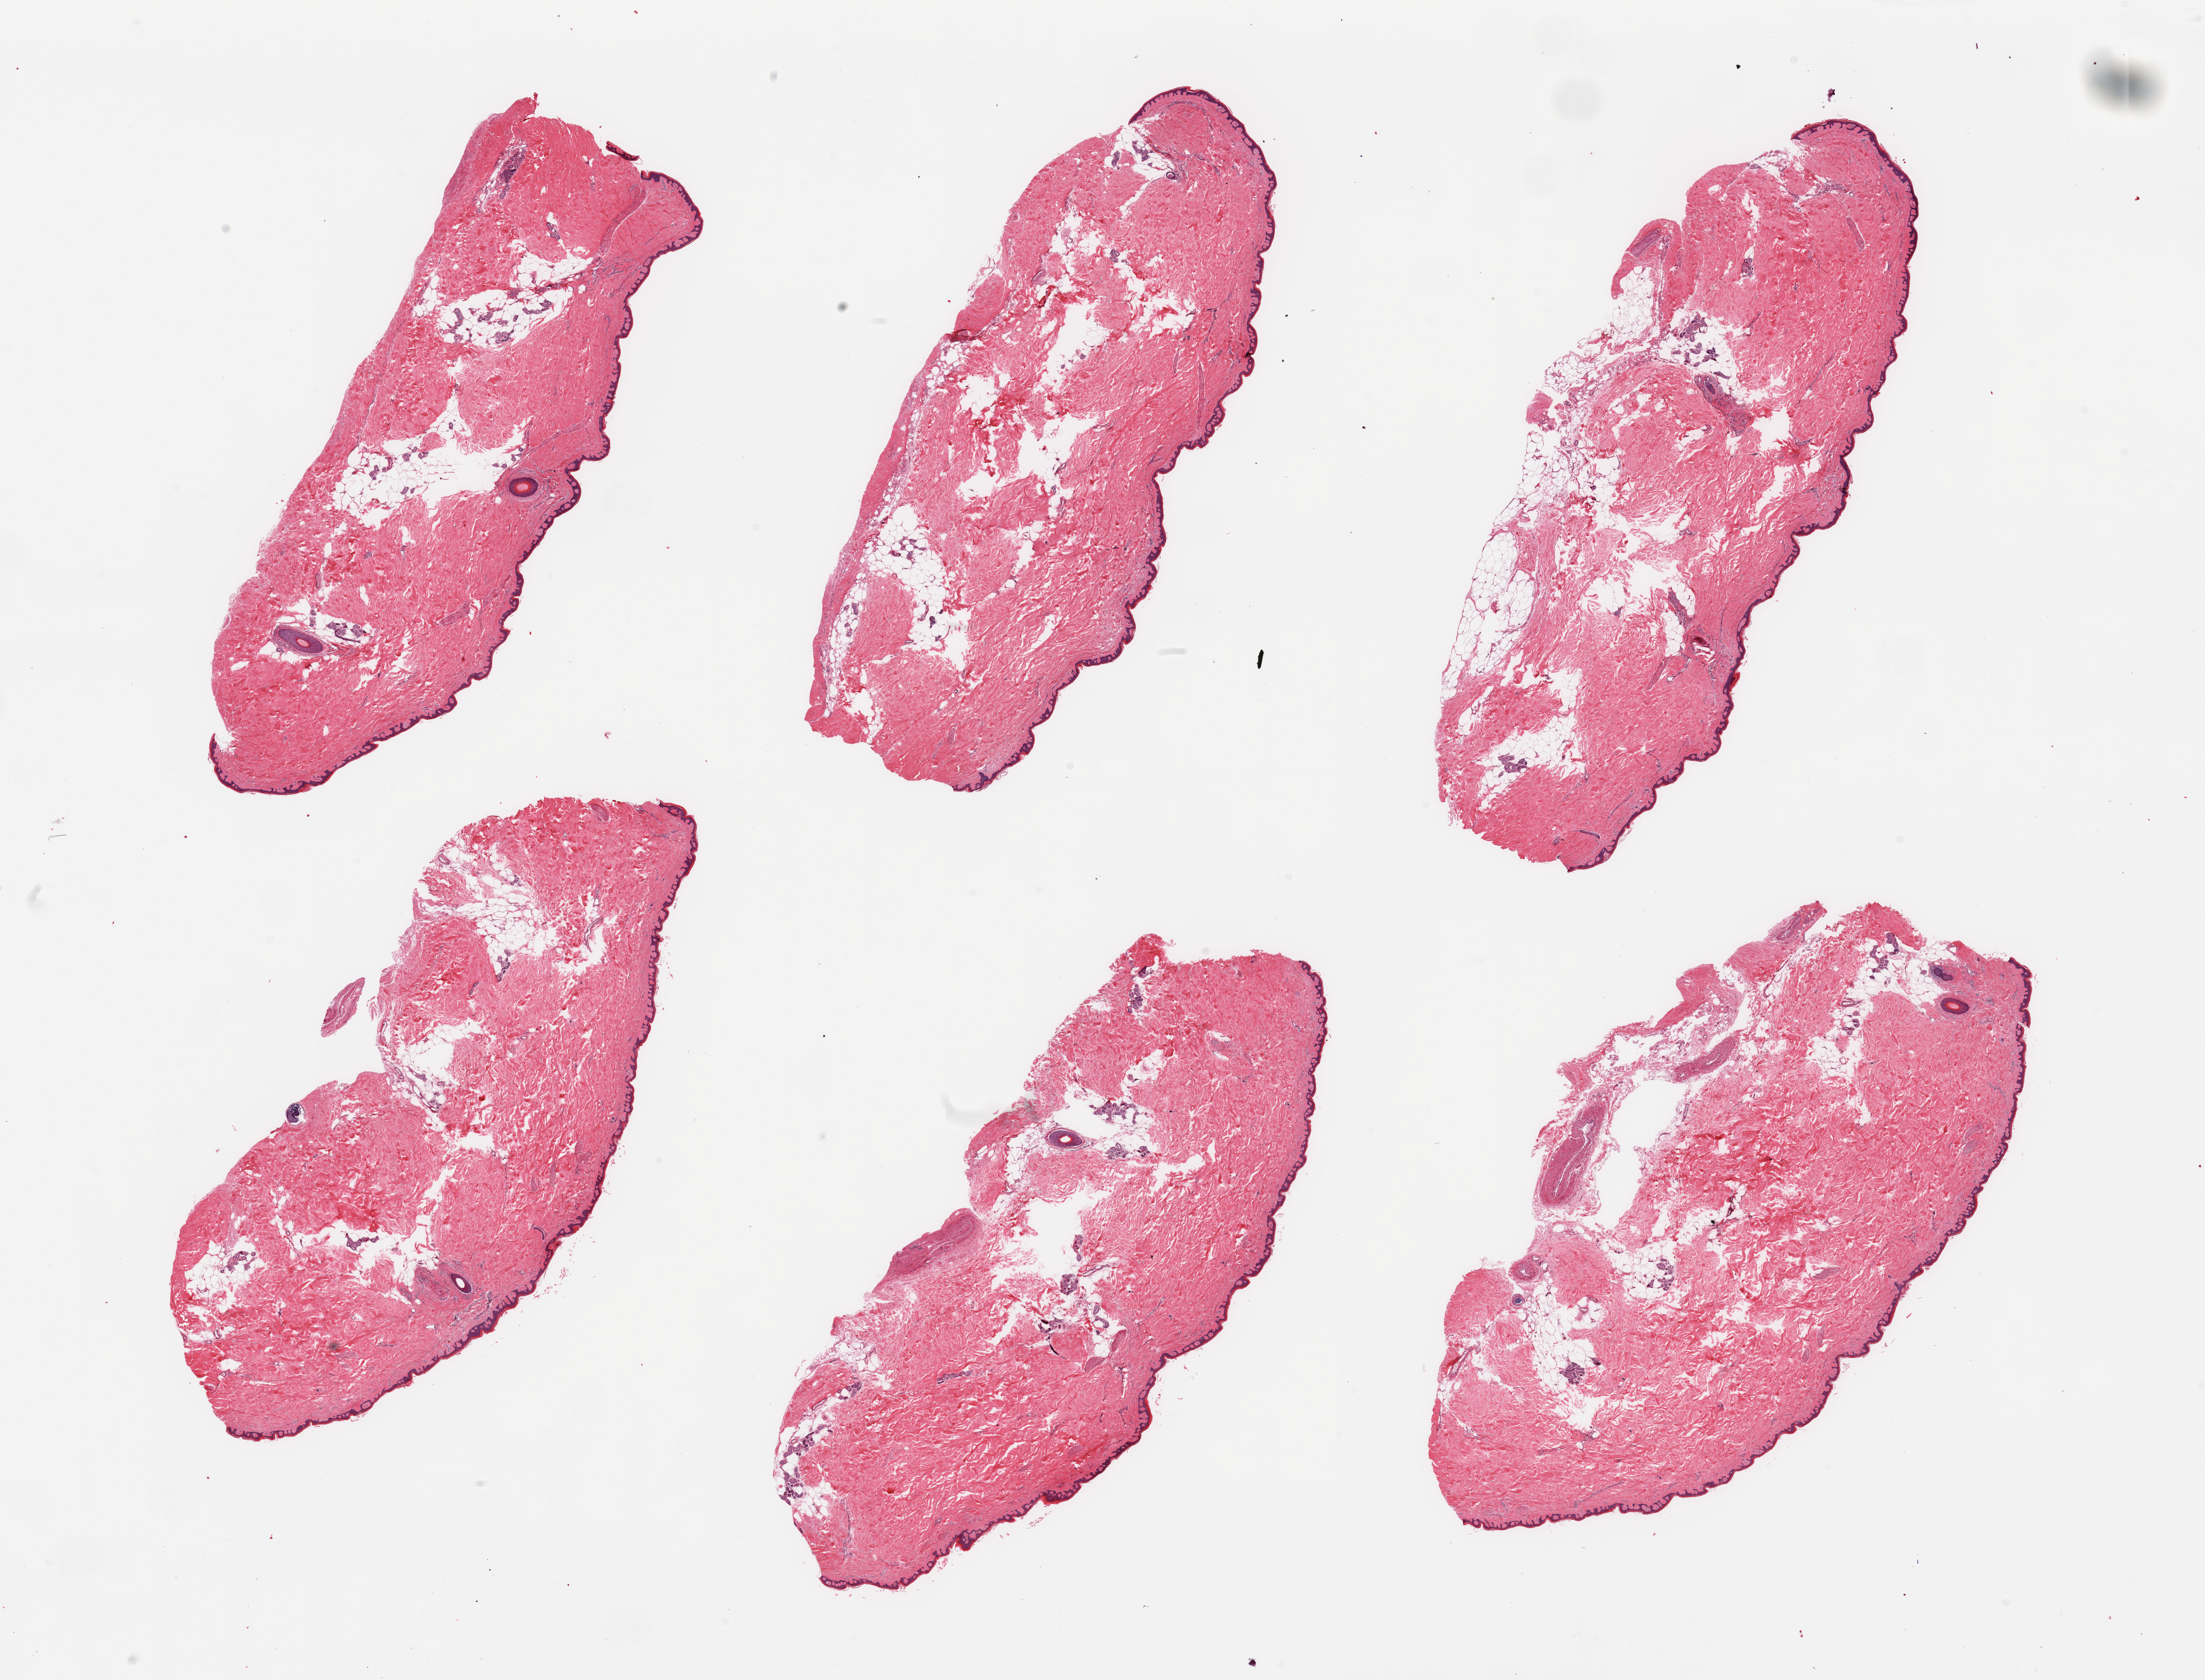
Whole-slide image, H&E stain, brightfield, low-resolution overview of the scanned area, about 27.6 x 21.0 mm (slide scanned at 20x). PAXgene-fixed paraffin-embedded (PFPE) section. Sampled site (target tissue): skin of lower leg. Tissue donor sample.
Pathologist's review note for this sample: 6 pieces, moderate interstitial dermal fat; squamous epithelium is ~30-40 microns.